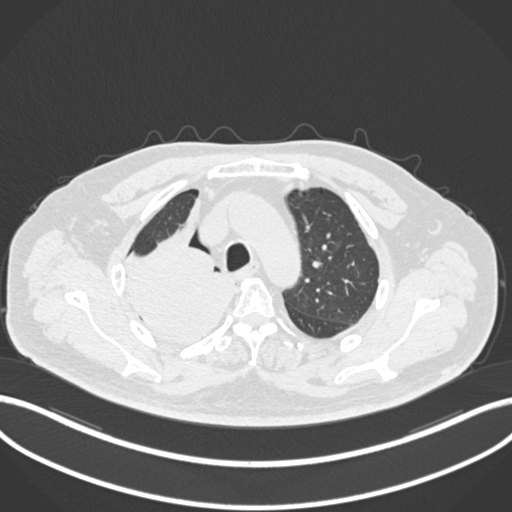
Chest CT, one axial slice; reconstruction kernel B30f; lung window (W 1500 / L -600 HU); 1 mm slice thickness; 512 × 512 image matrix, field of view 400 × 400 mm. Patient: male, 68 years. From the clinical record (not read from this slice): clinical TNM (as recorded): T2a N0 M0.
Annotated regions visible in this slice (bounding box drawn by a radiologist):
- lung tumour (recorded histology: adenocarcinoma): bounding box <123,202,235,345> (left, top, right, bottom; pixels)